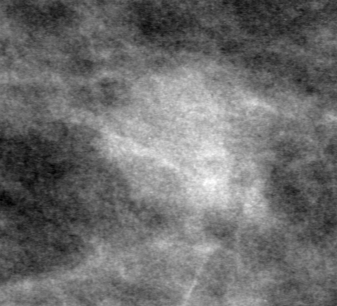
Region of interest cut from a scanned film mammogram (one marked finding), left breast, MLO view.
Mass, shape oval, margins obscured; BI-RADS assessment category 0 (incomplete: needs additional imaging); pathology result (as recorded, not read from the image): benign.